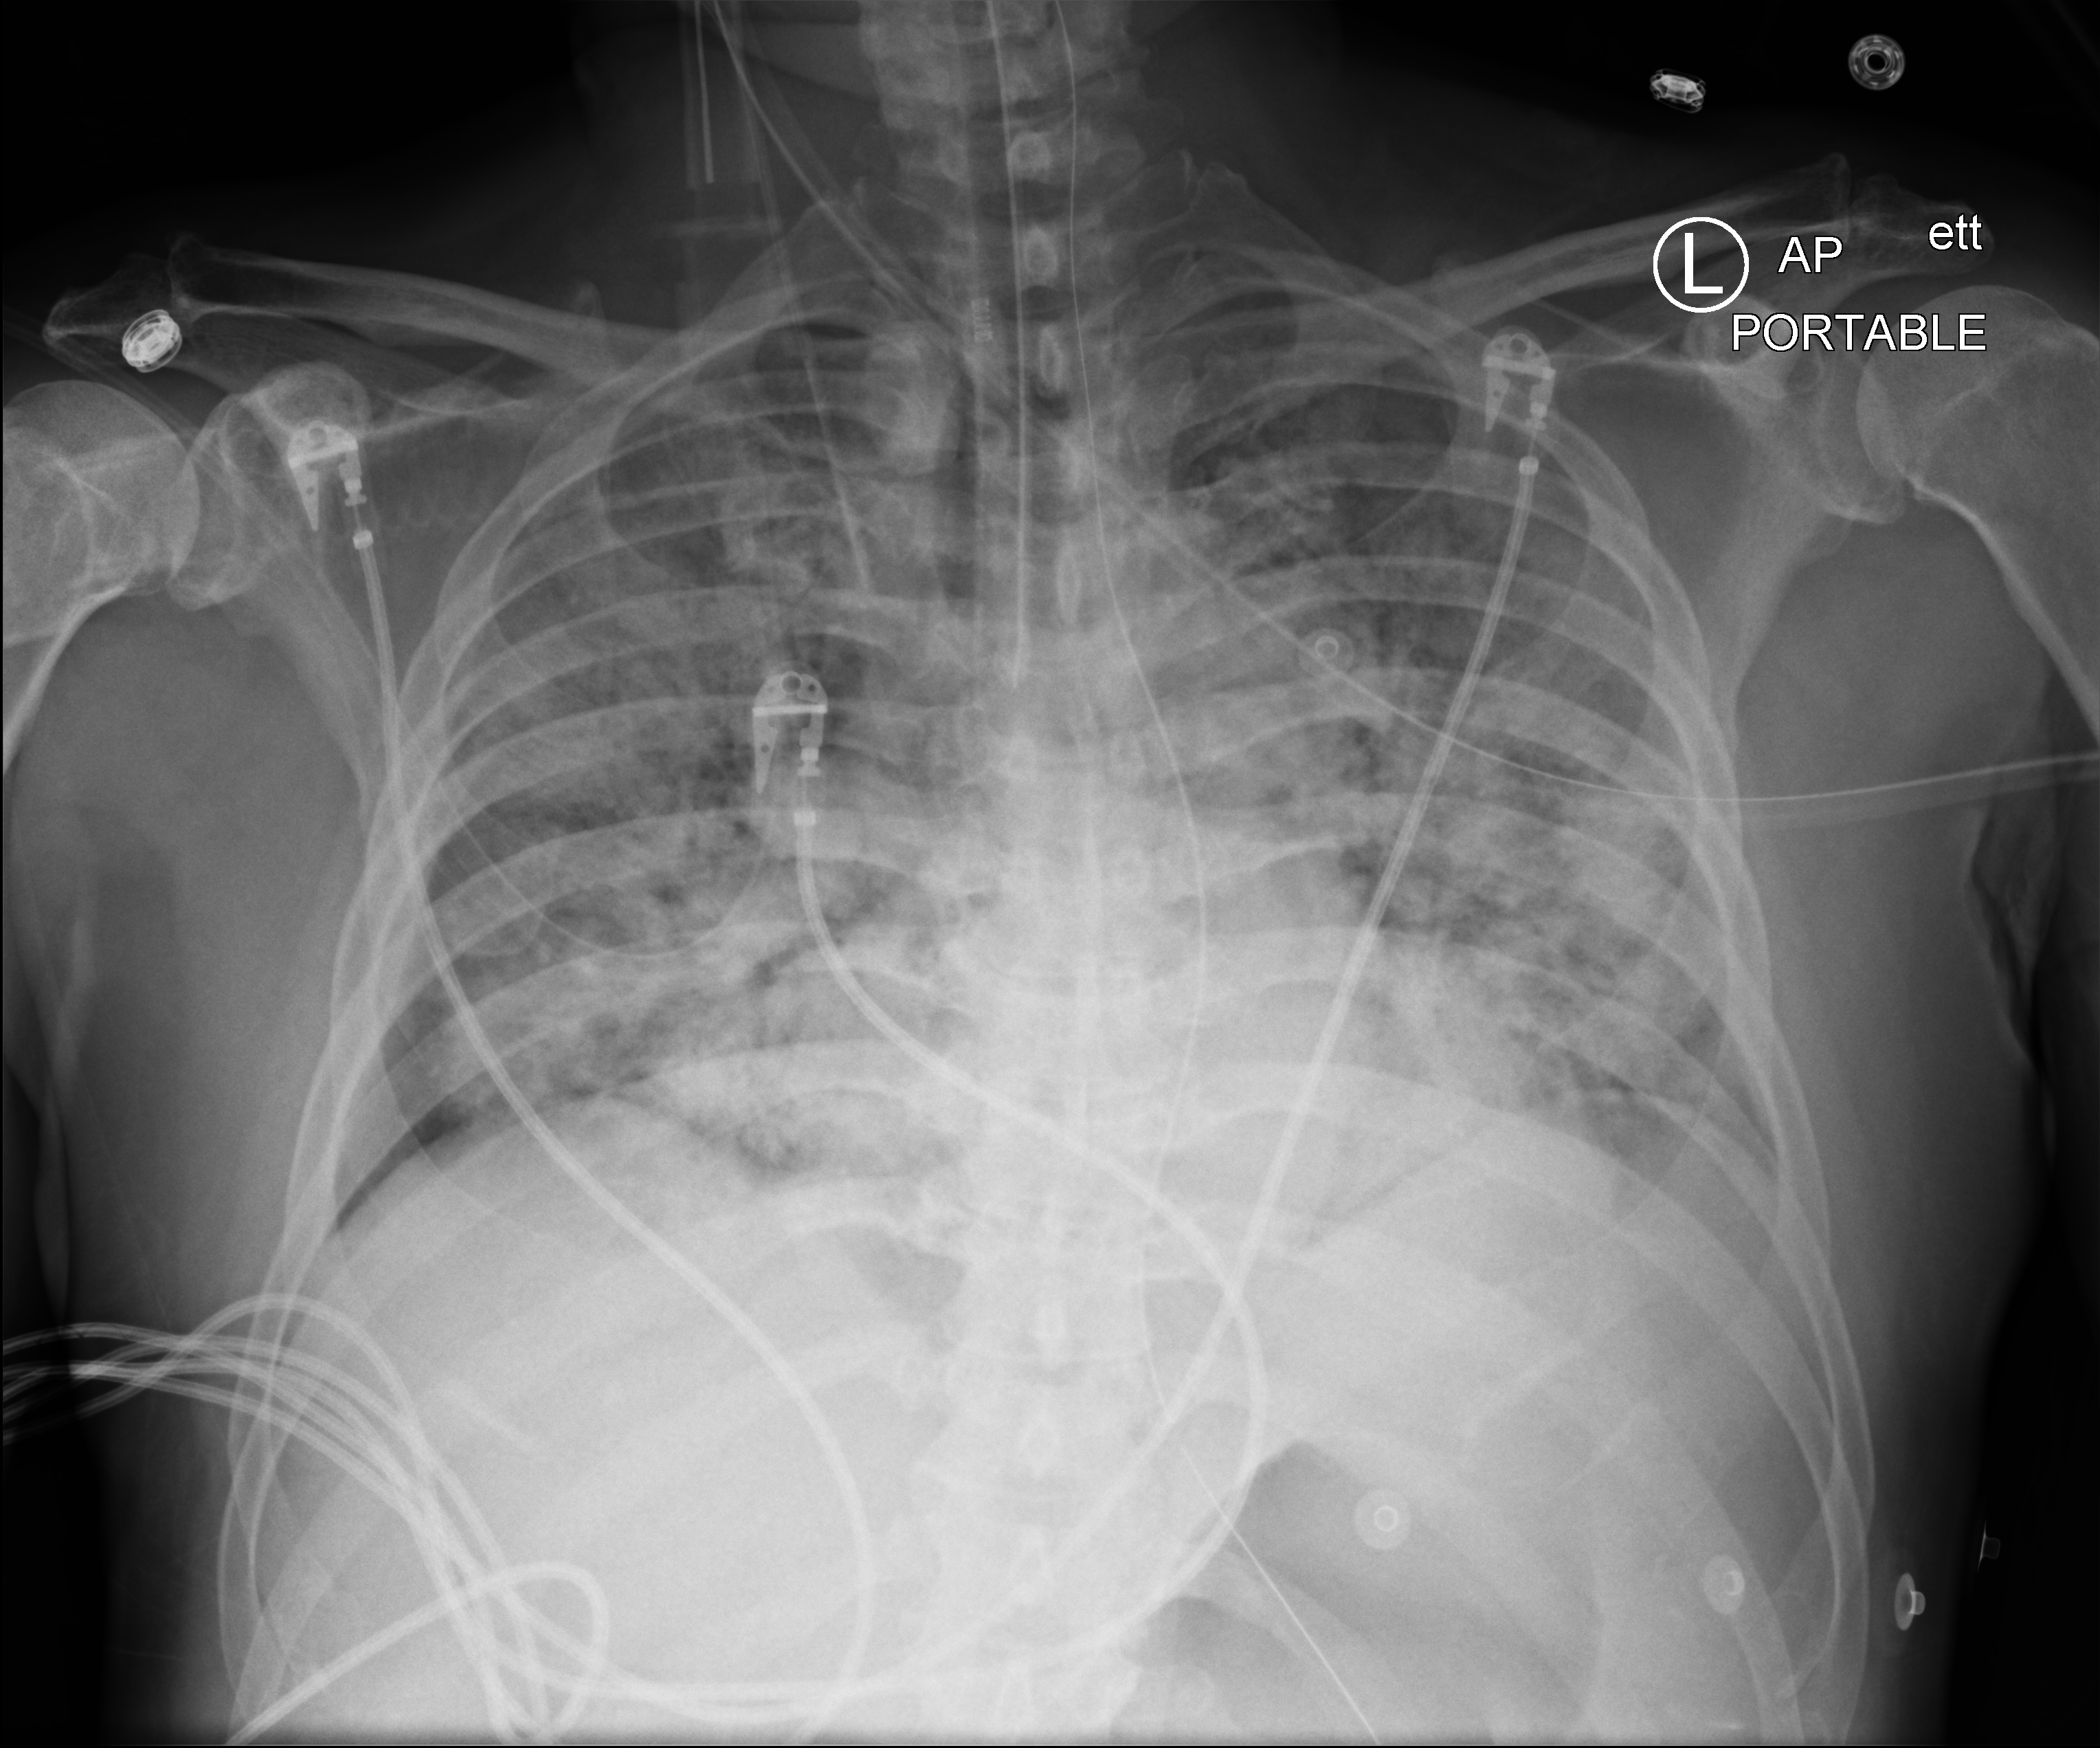
Bedside chest radiograph (computed radiography), anteroposterior (AP) projection. Patient hospitalised with COVID-19; male, aged 60–74 years.
From the hospital-stay record, not from the radiograph (when in the stay this image was taken is not recorded): hypertension (admission record): yes.